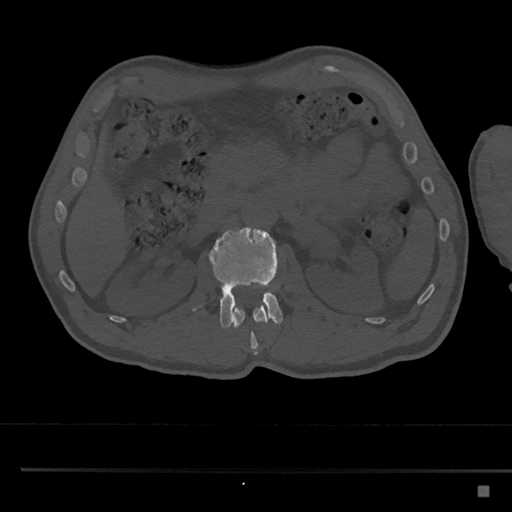
CT including the spine, one axial slice. Position 787 of 797 along the scan axis. 120 kVp. Bone window (W 1800 / L 400 HU). 0.5 mm slice thickness. 512 × 512 image matrix. Patient: male, 59 years. From the clinical record (not read from this slice): primary cancer: prostate.
Structures marked on this image (semi-automatically segmented with operator editing):
- L1 vertebra: box from (x=233, y=302) to (x=269, y=354) px
- L2 vertebra: (x=191, y=226)–(x=283, y=328)